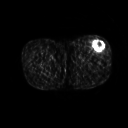
FDG PET of an extremity soft-tissue mass (from a PET/CT study), one axial slice. Slice 225 of 267 in the series (ordered by position). 3.27 mm slice thickness. 128 × 128 image matrix, field of view 500 × 500 mm. Patient: male, 64 years. From the clinical record (not read from this slice): histological type: extraskeletal osteosarcoma; grade: high; site of the primary tumour: thigh.
Structures marked on this image (expert contour drawn on MRI and transferred to this co-registered scan by the dataset authors):
- gross tumour volume (mass): bounding box (x1, y1, x2, y2) in pixels: (92, 41, 105, 52)